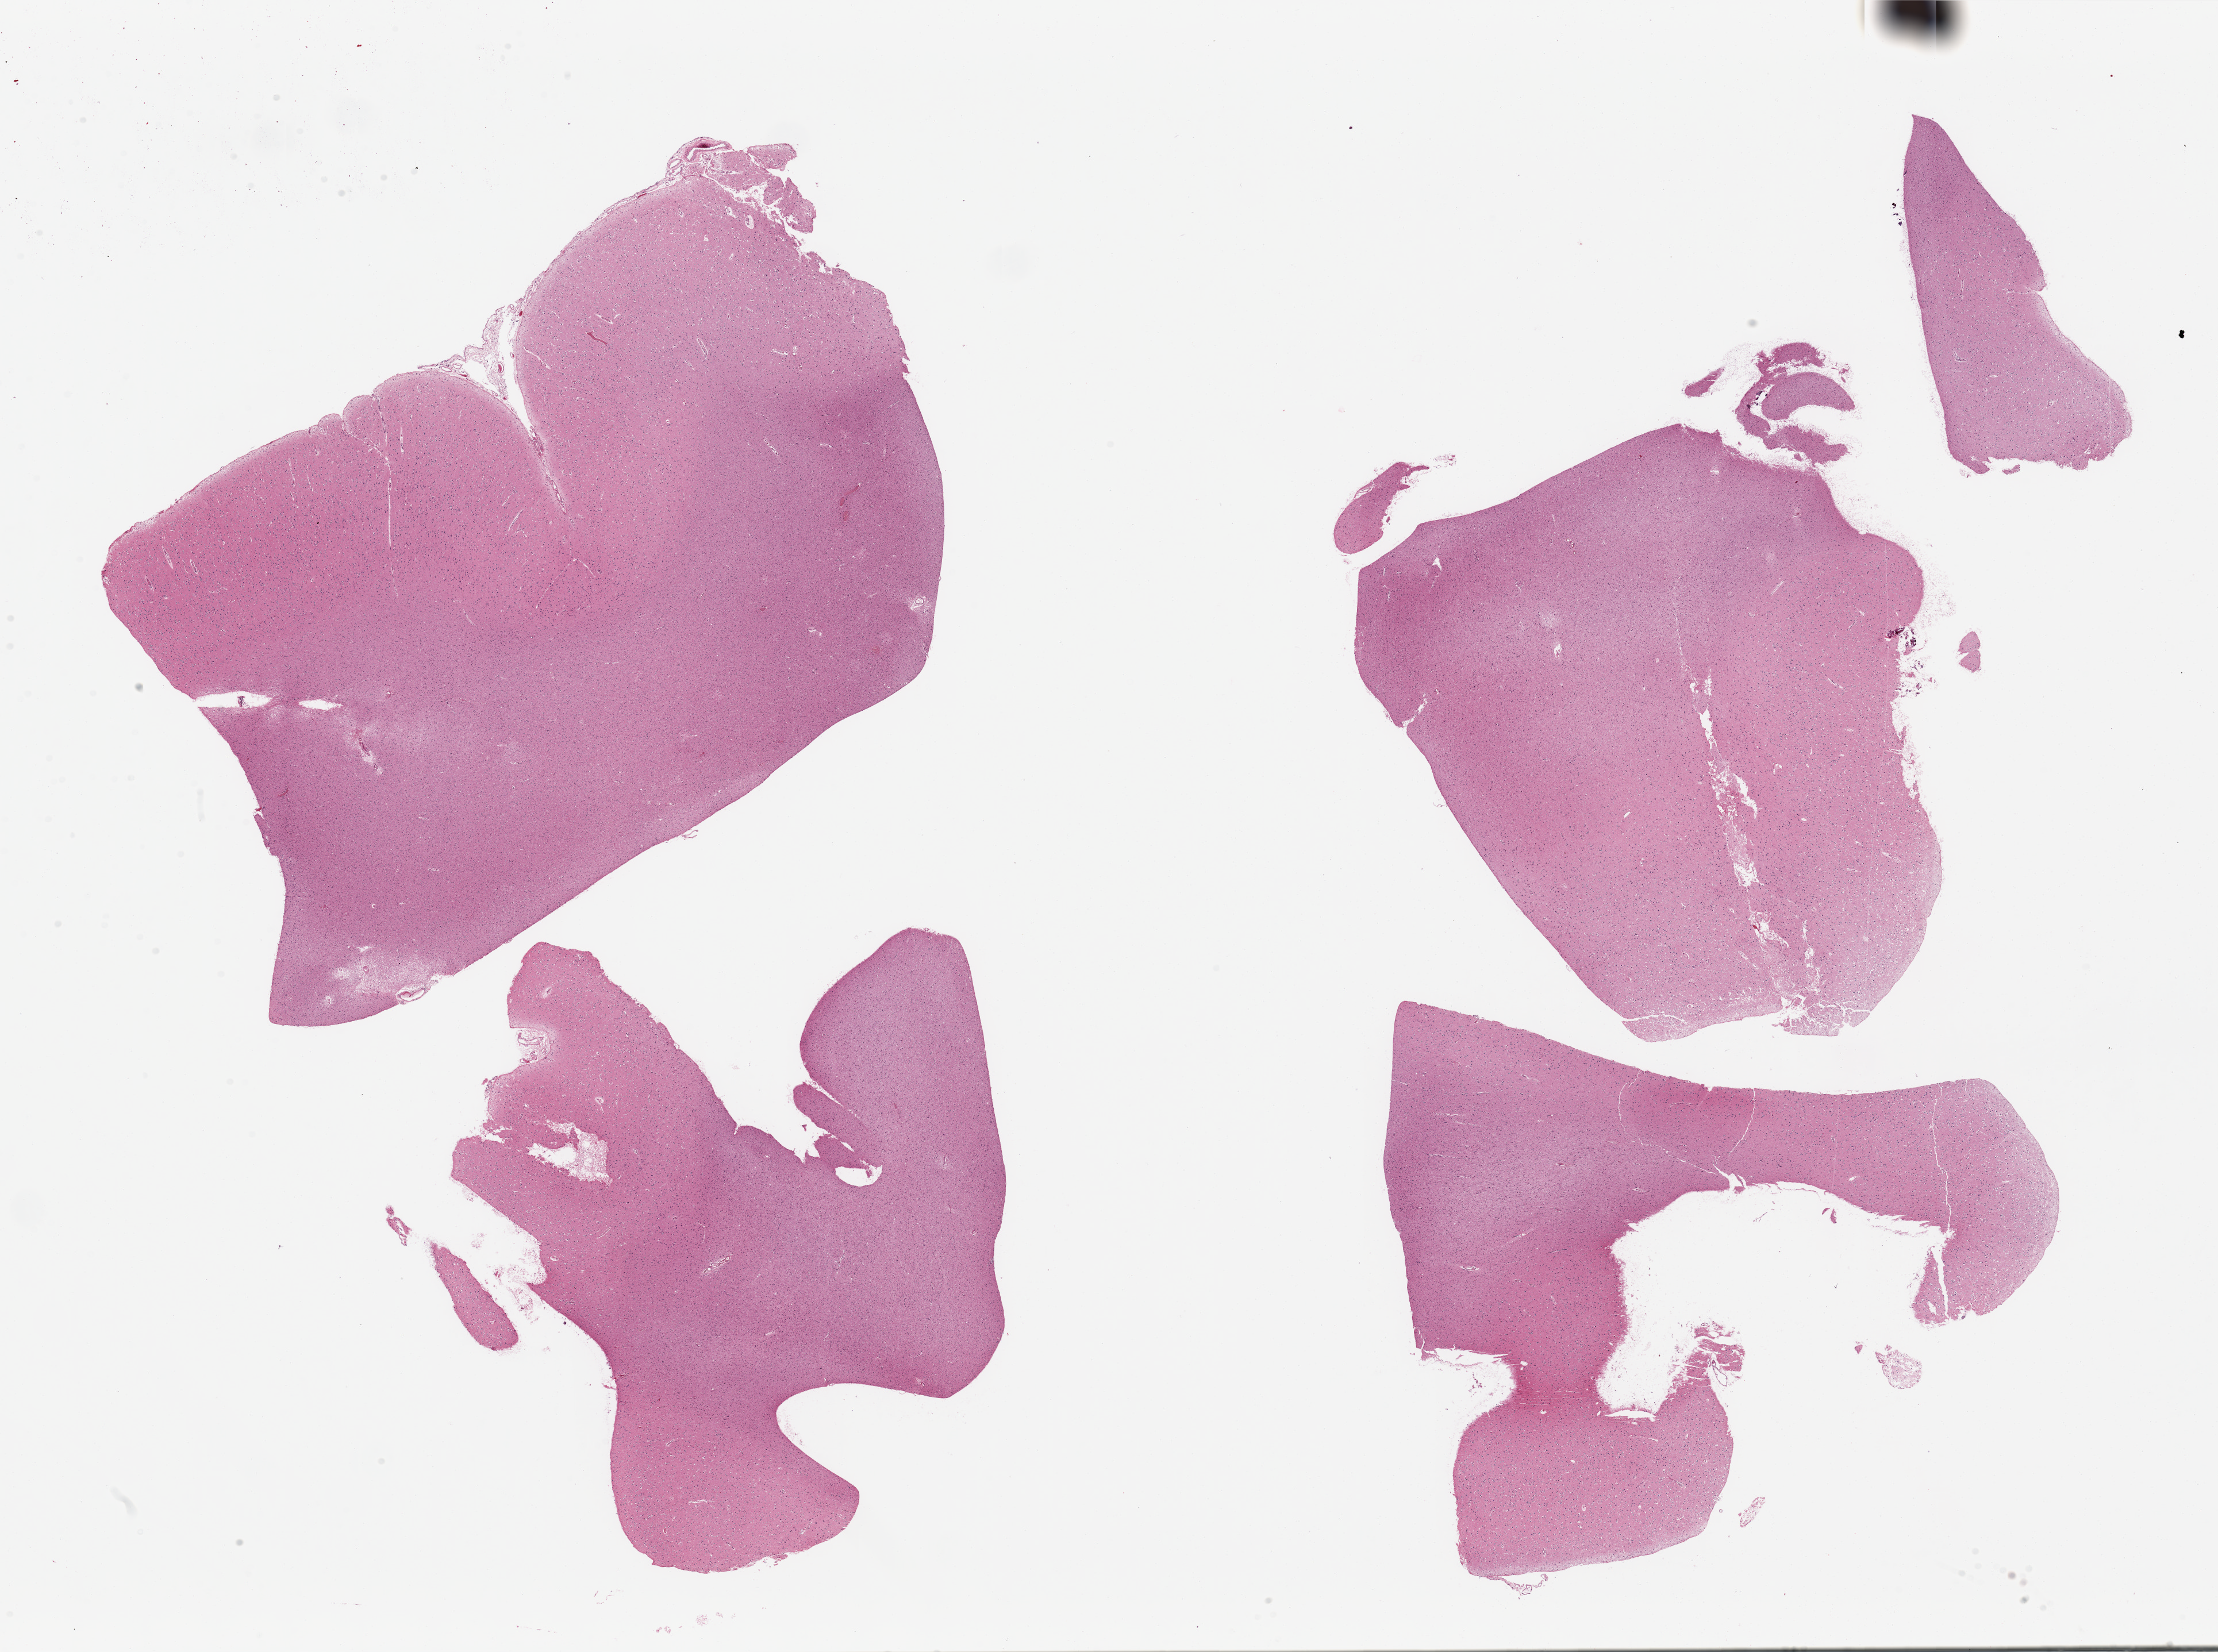
Whole-slide image, haematoxylin and eosin stain — low-resolution overview of the scanned area, about 30.5 x 22.7 mm (slide scanned at 20x); PAXgene-fixed paraffin-embedded (PFPE) section; sampled site (target tissue): cerebral cortex; tissue donor sample. Donor sex: male.
- reviewer comment on this tissue sample: 4 pieces